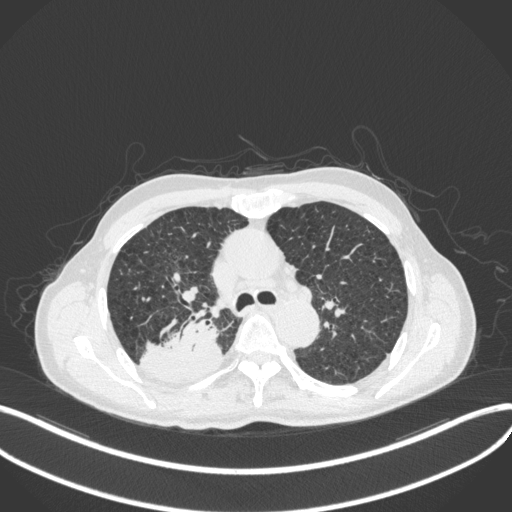
Chest CT, one axial slice; 120 kVp; lung window (W 1500 / L -600 HU); 1 mm slice thickness; 512 × 512 image matrix, field of view 400 × 400 mm. Male patient, age 79 years. Case-level facts recorded for this patient, not image findings: clinical TNM (as recorded): T3 N0 M0.
Outlined on this slice (rectangle marked by the reading radiologist):
- lung tumour (recorded histology: adenocarcinoma): bounding box <139,307,224,384> (left, top, right, bottom; pixels)